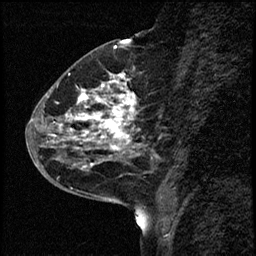
Breast MRI (dynamic contrast-enhanced), one sagittal slice; position 24 of 68 along the scan axis; dynamic contrast-enhanced study with each time point stored as its own series, time point 2 of 3 at this slice position (early post-contrast, ordered by acquisition time); 1.5 T; TE 4.2 ms, TR 17.6 ms; 256 × 256 image matrix, field of view 200 × 200 mm. Female patient, age 52 years. Case-level facts recorded for this patient, not image findings: setting: breast cancer imaged before/during neoadjuvant chemotherapy; receptor status: HER2-positive.
Structures marked on this image (semi-automatic segmentation, software-assisted and operator-edited):
- analysis volume of interest (the breast-tissue region the enhancement analysis was run in; not a lesion): box from (x=50, y=61) to (x=158, y=184) px
- tumour enhancement mask (voxels above the 100 % enhancement threshold inside the analysis volume of interest): (x=54, y=73)–(x=140, y=168)